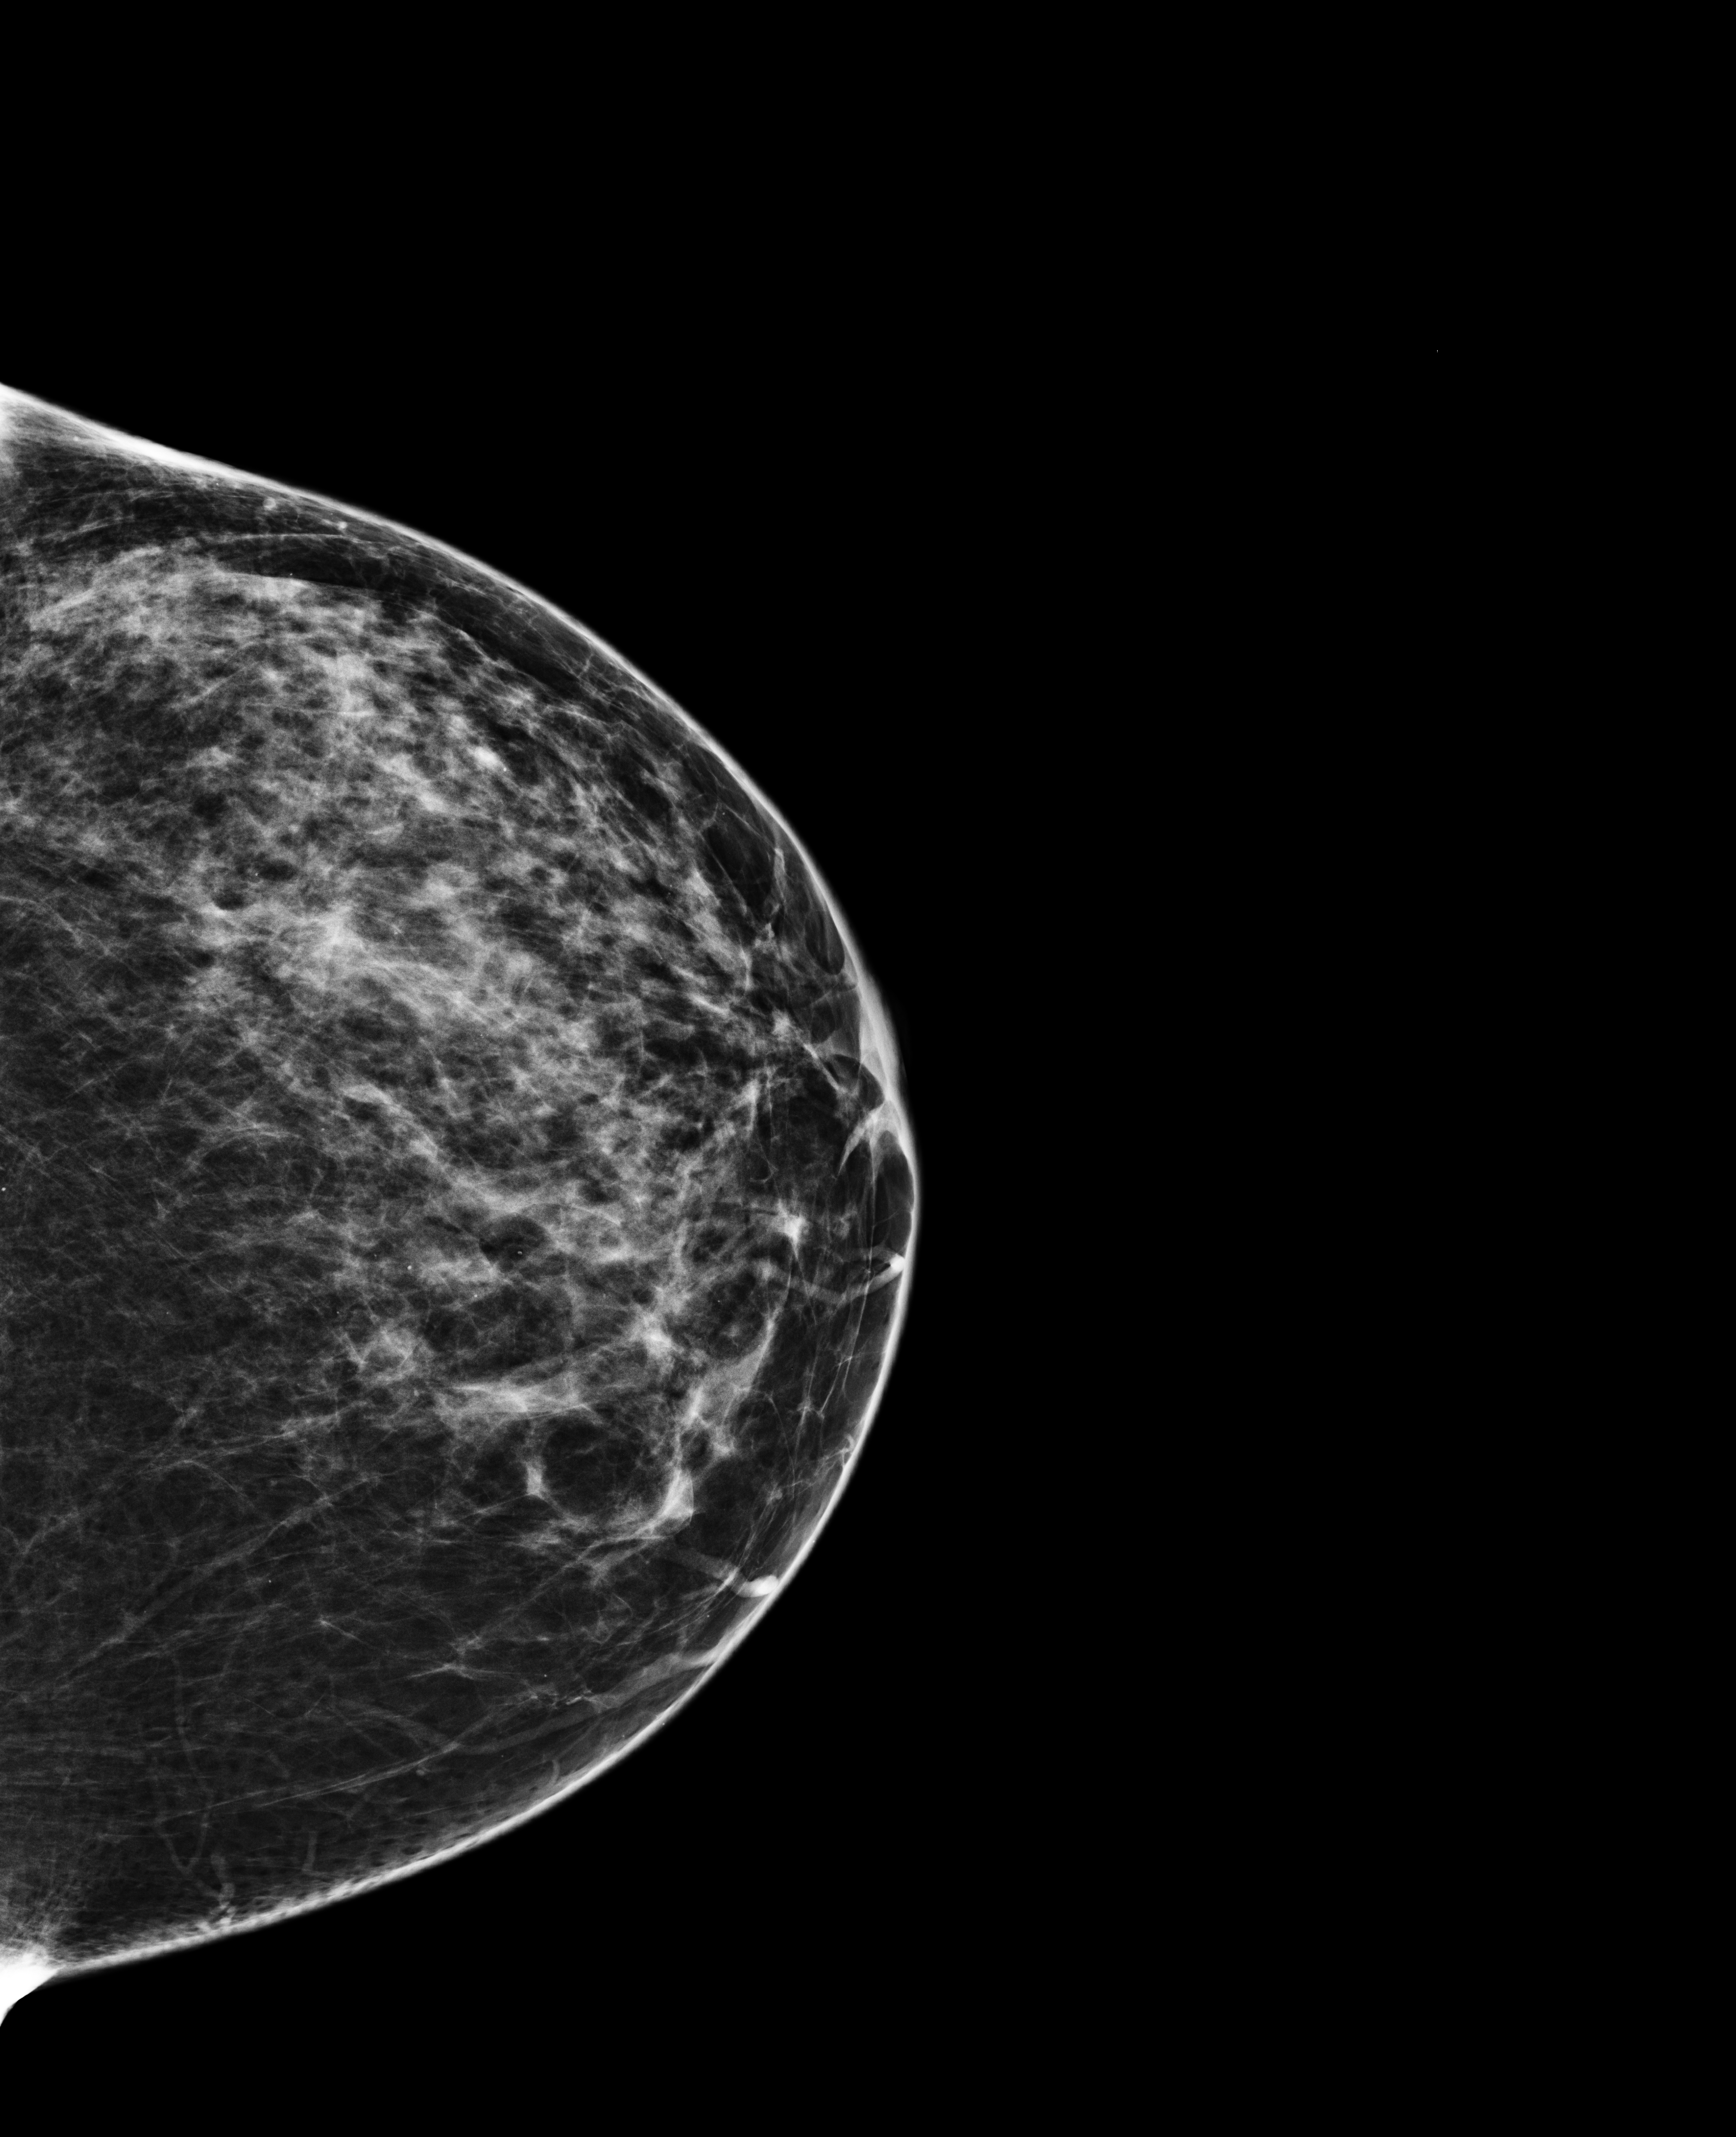
Digital mammogram (FFDM); left breast; cranio-caudal projection; annual screening mammography examination; system: Selenia Dimensions. Patient aged 47 years (female).
BI-RADS breast density category at the screening exam (both breasts, scale 1–4): 3. Final BI-RADS category for the screening round (tomosynthesis exam, both breasts): category 1. Recall: no recall after this screen.